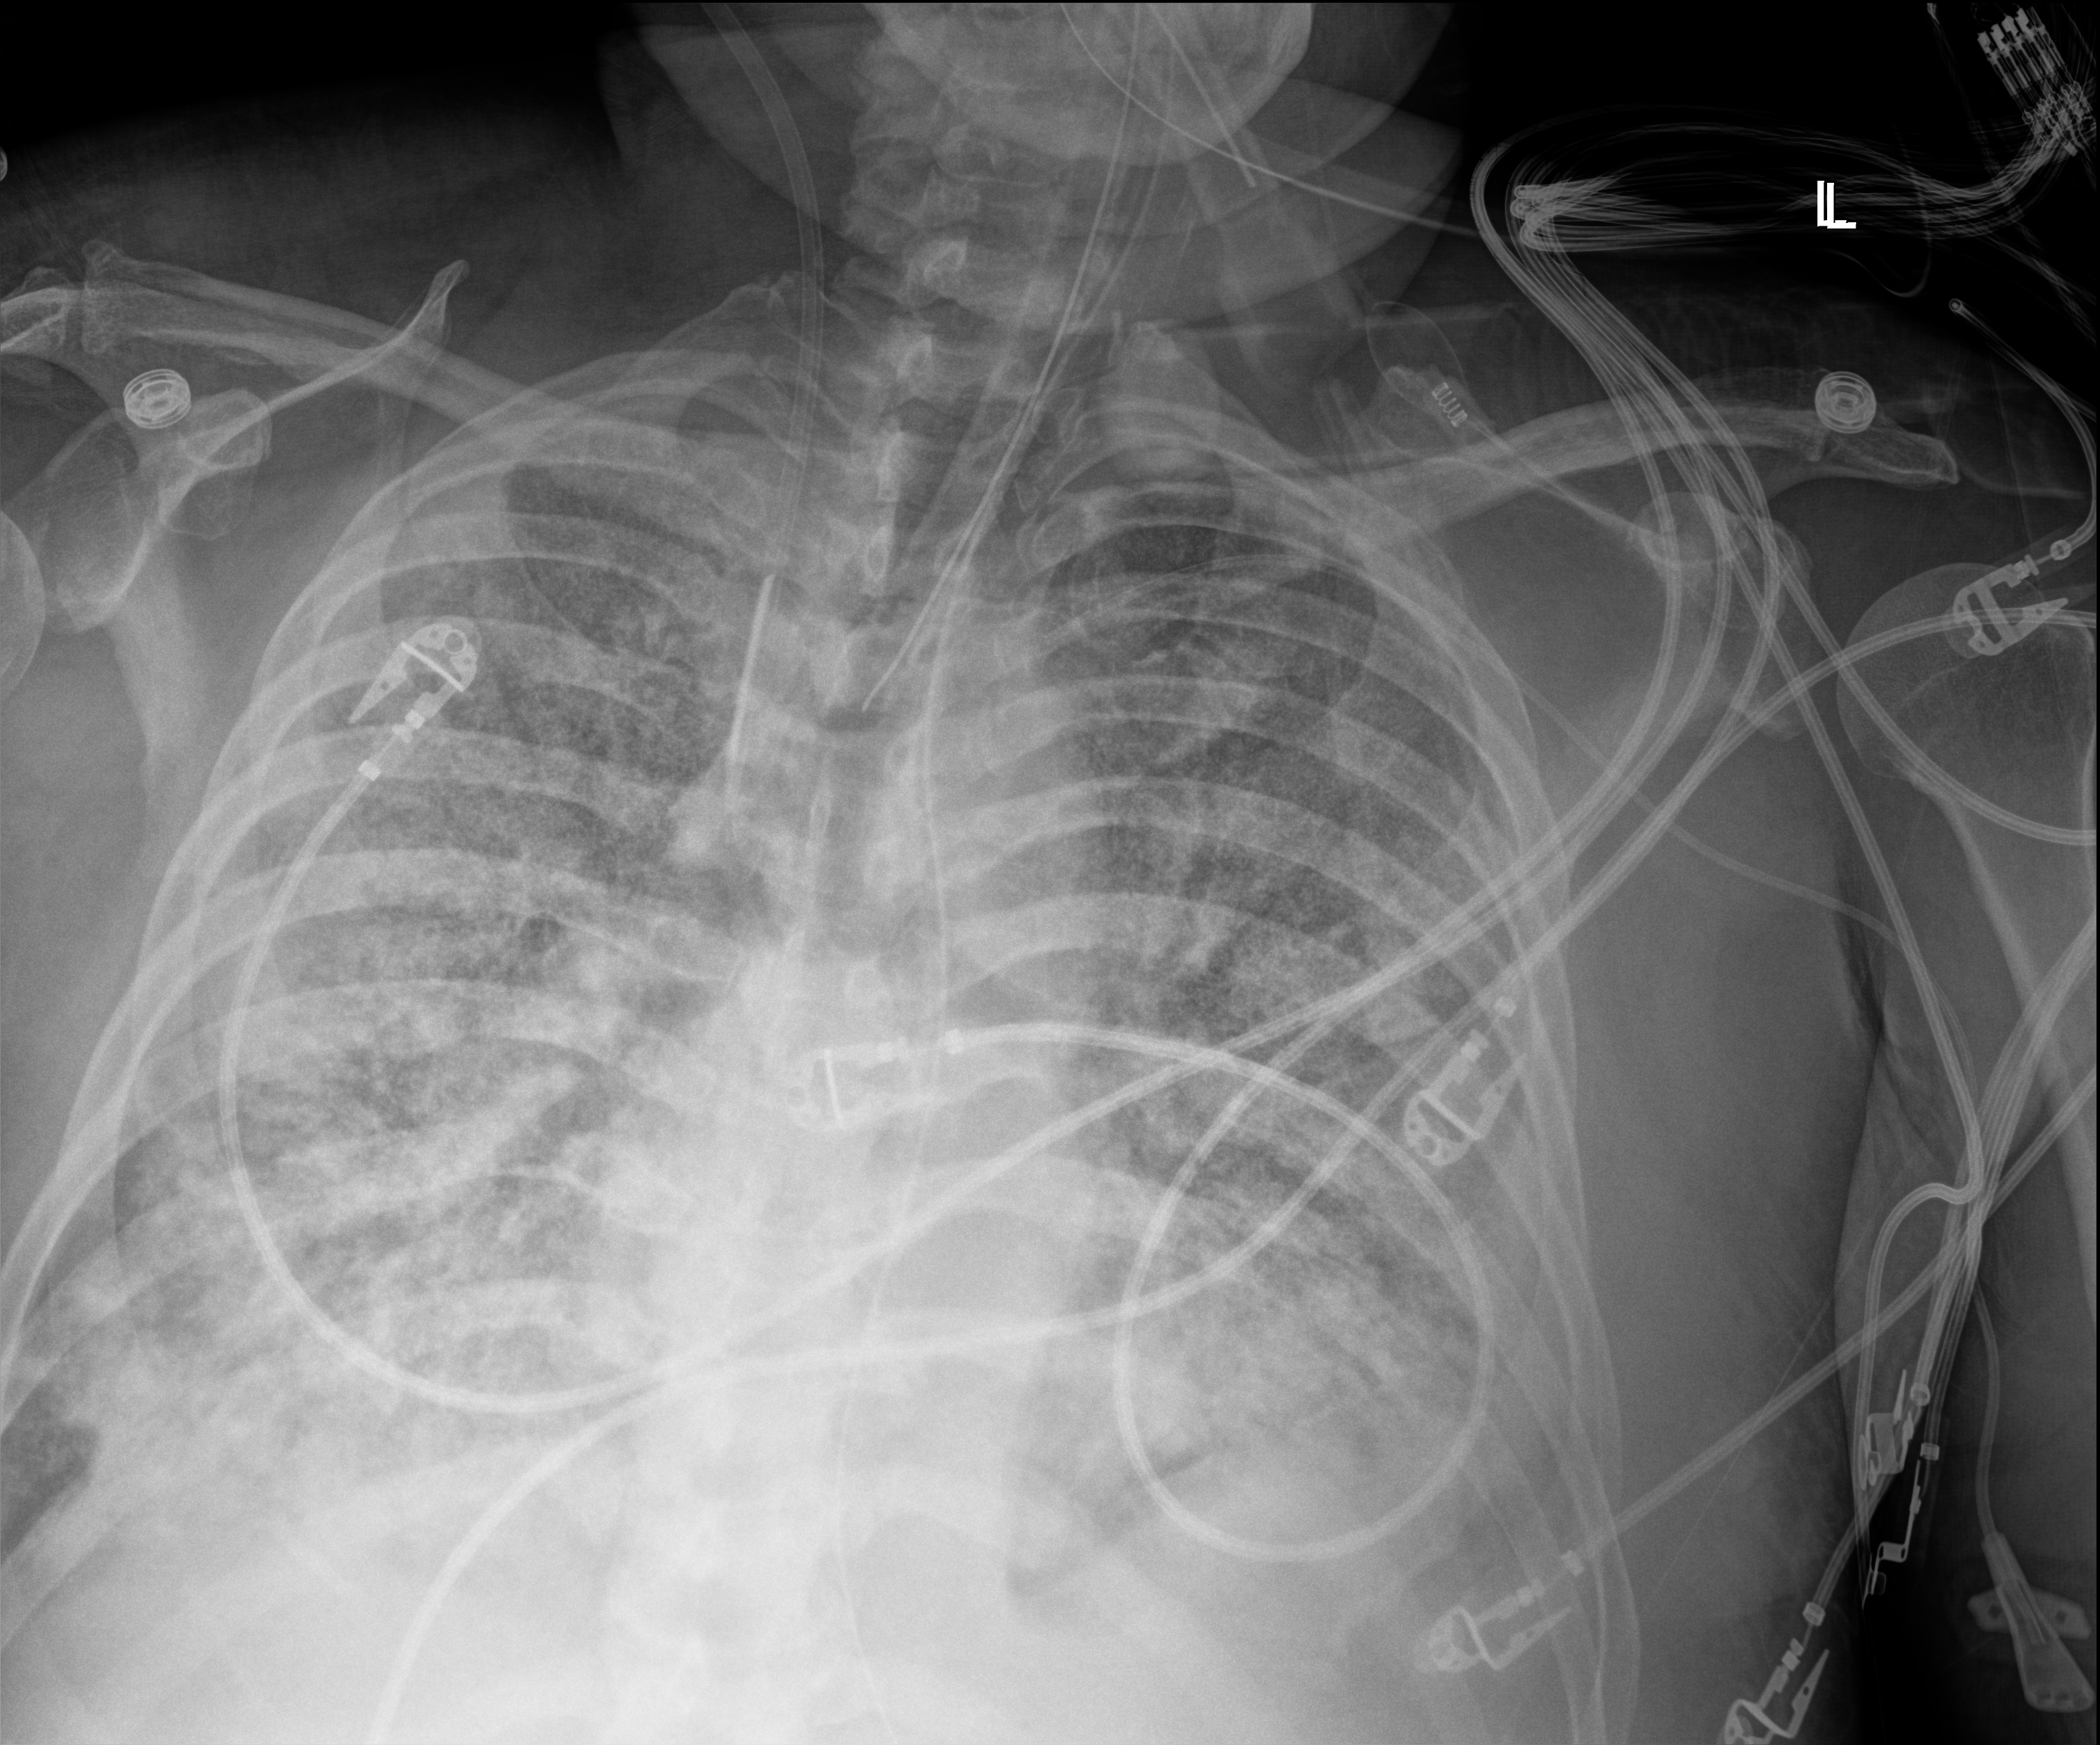
Portable chest radiograph, anteroposterior (AP) projection. Male patient hospitalised with COVID-19, age 60–74 years.
Admission-level facts for this patient (not findings on this image; timing relative to this image not recorded):
- admitted to intensive care during this hospital stay: yes
- chronic kidney disease (admission record): no